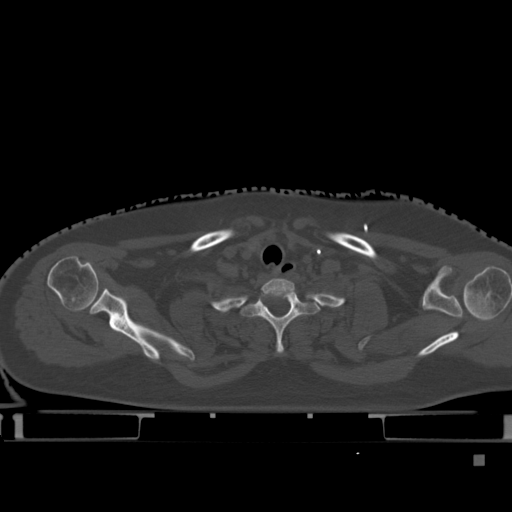
CT including the spine, one axial slice. Position 372 of 495 along the scan axis. Bone window (W 1800 / L 400 HU). 1.5 mm slice thickness. 512 × 512 image matrix. Patient: female, 33 years. Case-level facts recorded for this patient, not image findings: primary cancer: breast.
Annotated regions visible in this slice (semi-automatically segmented with operator editing):
- T1 vertebra: box from (x=242, y=288) to (x=320, y=354) px